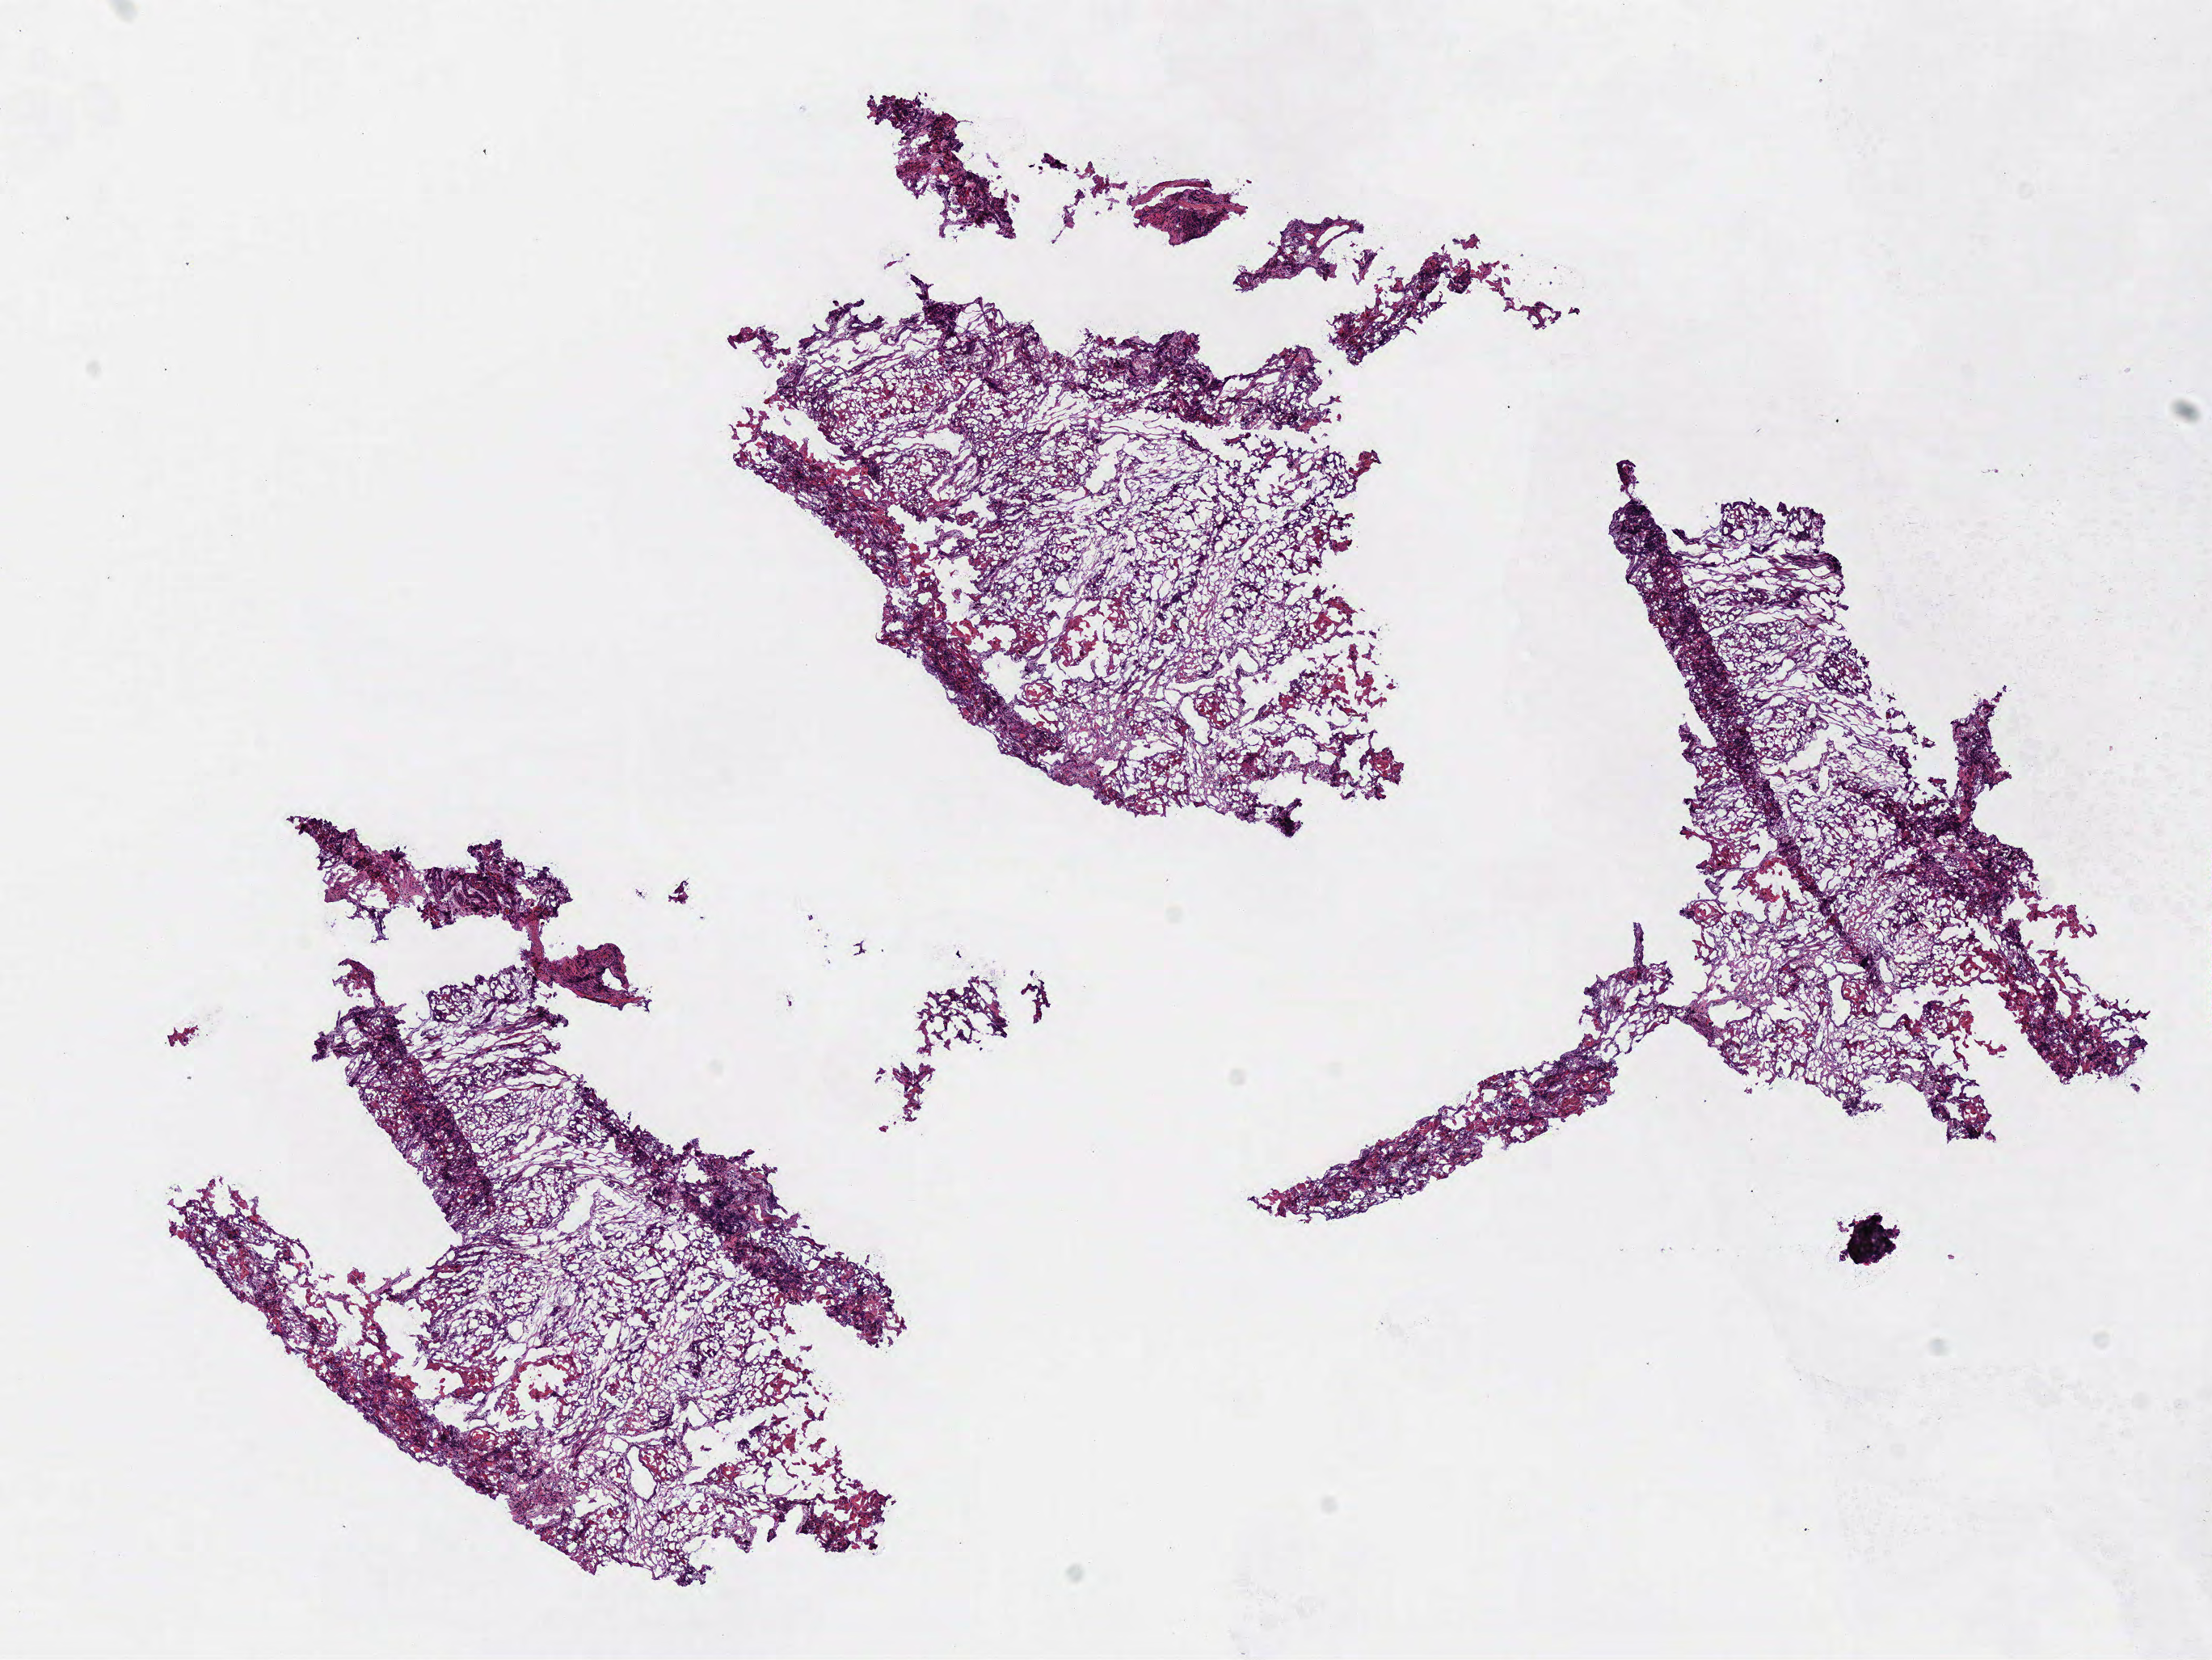
Whole-slide histology image, H&E-stained, a low-resolution overview of the entire scanned area, about 10.8 x 8.1 mm (acquisition: 40x scan); frozen section; head and neck, primary tumour sample. Patient: male, age at initial diagnosis 66 years. Histologic grade: G2 (moderately differentiated). Pathologist review of this section (percent, as recorded): tumour cells 85%, tumour nuclei 80%, normal cells 0%, stromal cells 15%, necrosis 0%.
- AJCC pathologic stage: IVA
- histologic diagnosis: Squamous cell carcinoma, NOS (tongue, NOS)
- TNM: T3 N2b